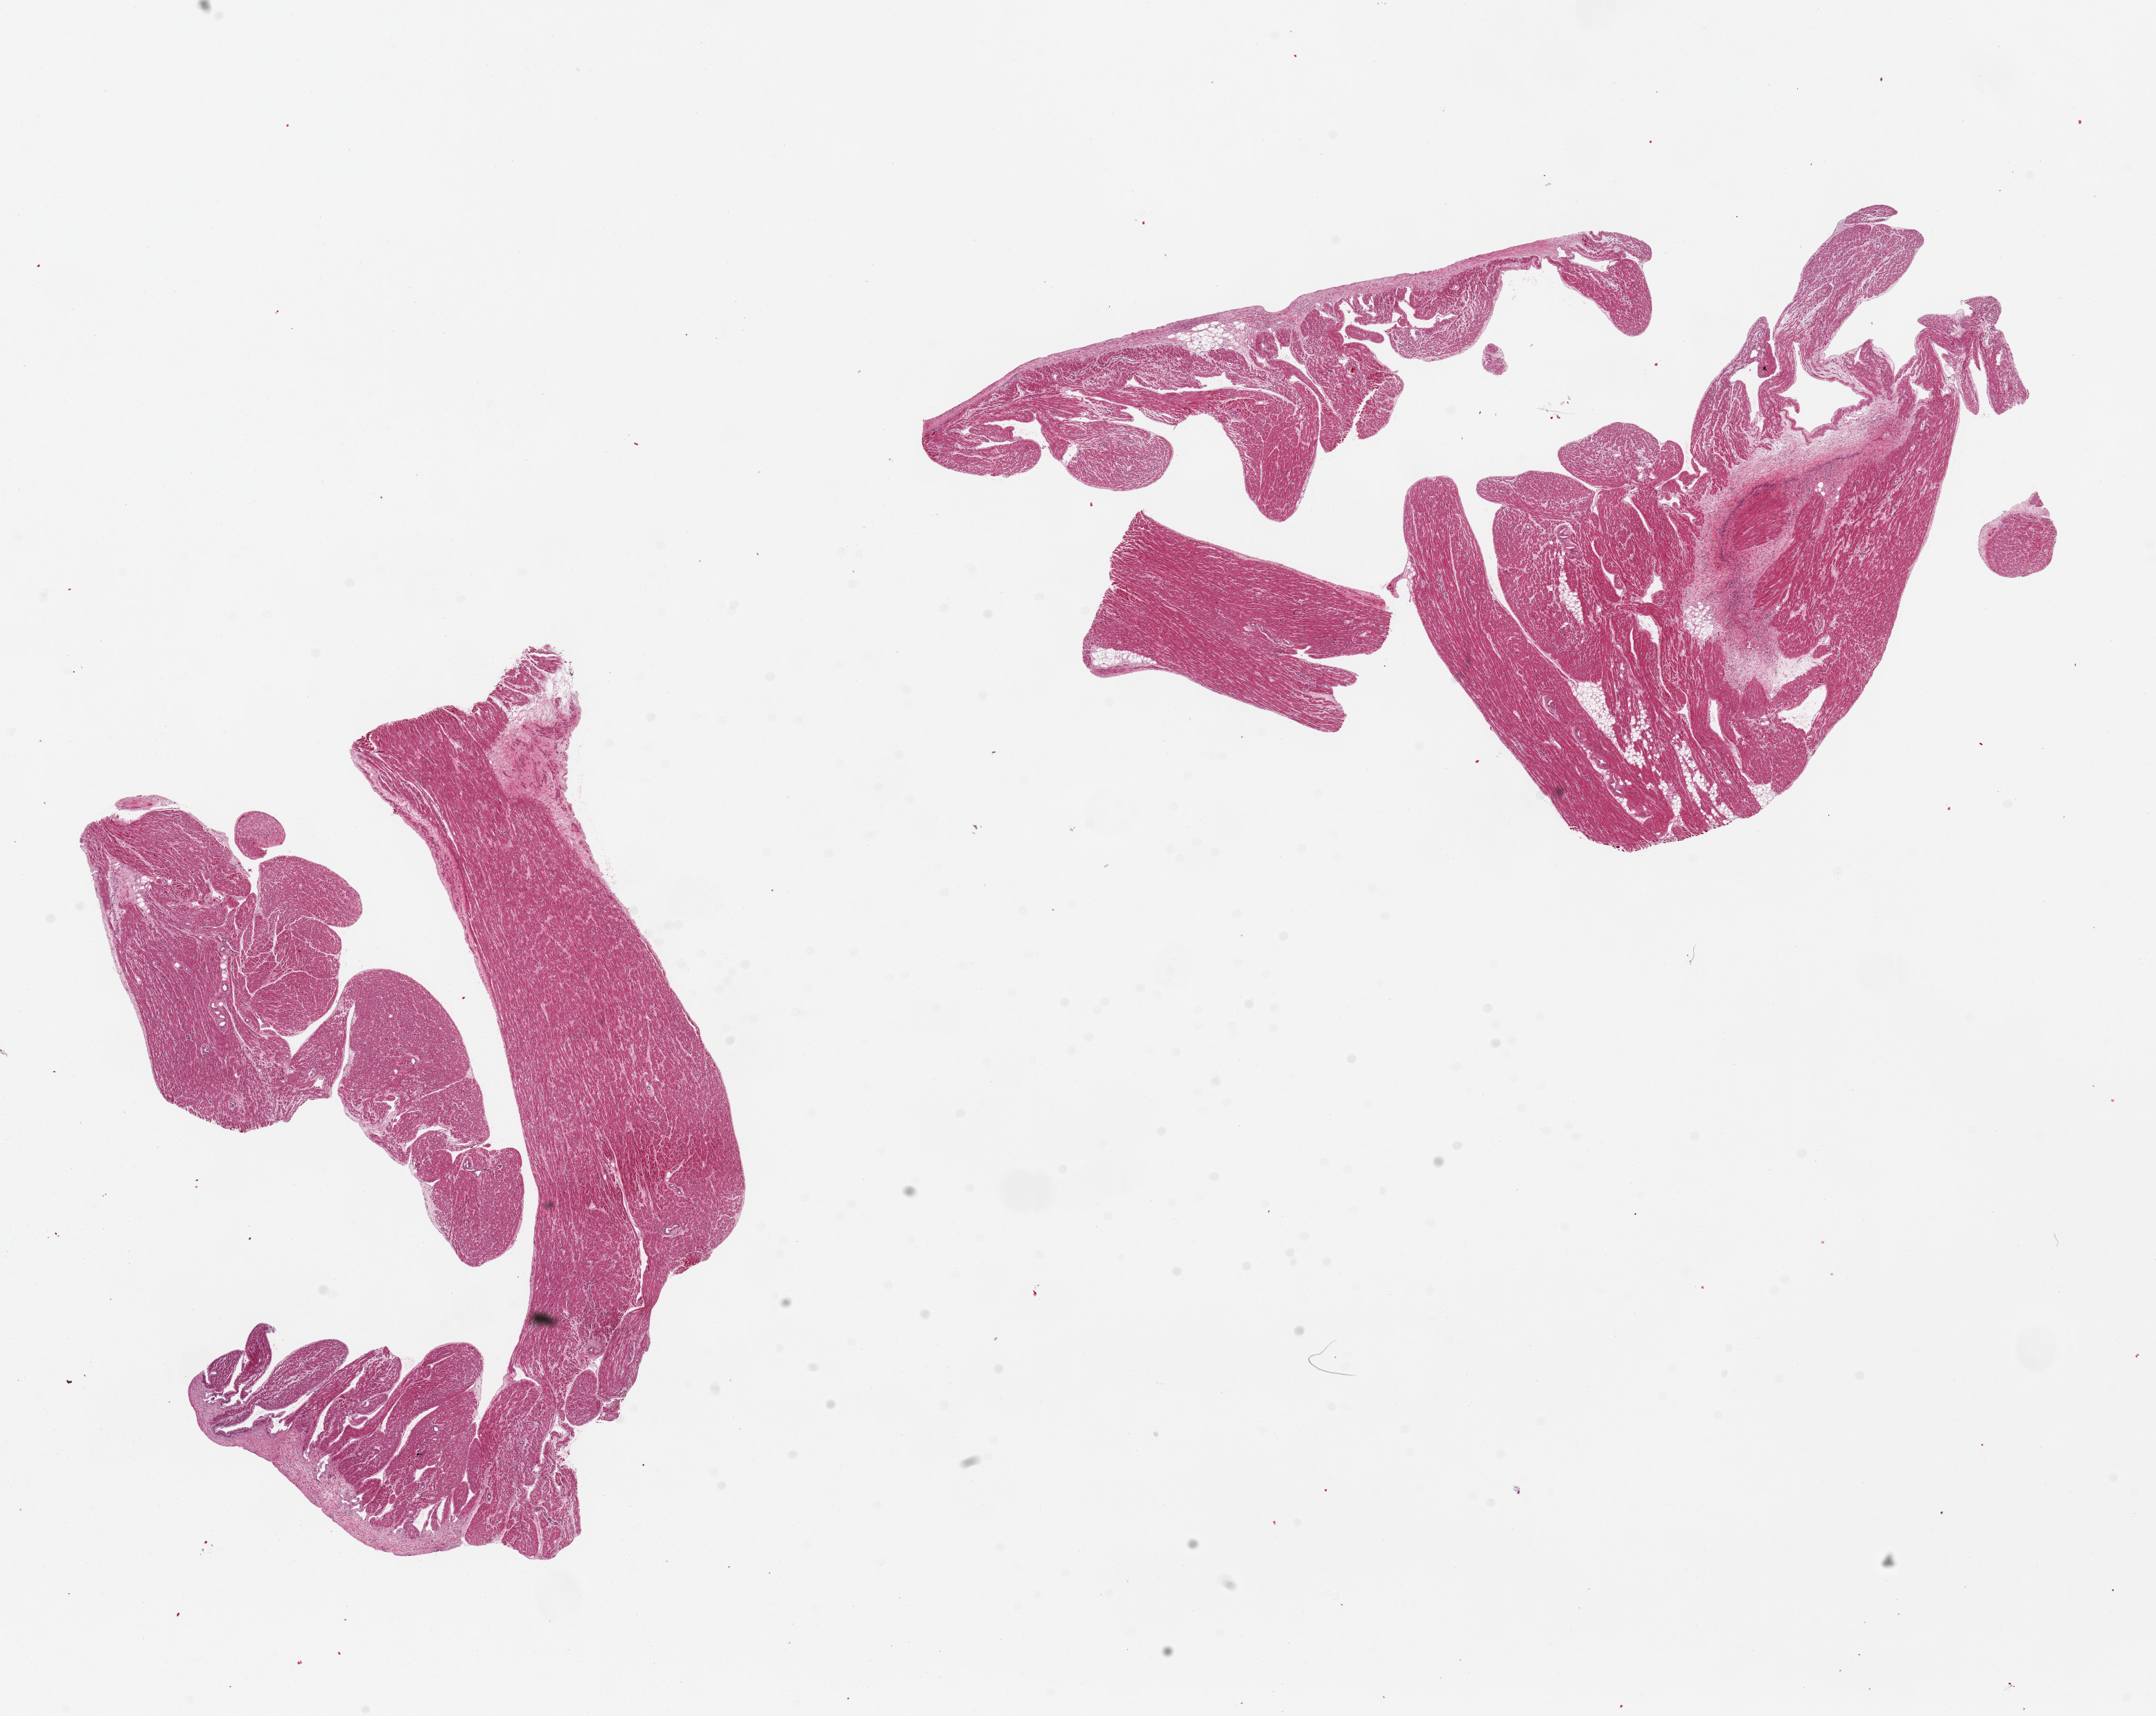
Digitized H&E-stained section — shown as a low-resolution overview of the whole scanned area (about 24.6 x 19.6 mm, acquisition: 20x scan). PAXgene-fixed paraffin-embedded (PFPE) section. Section of auricular appendage (target tissue). Donor tissue sample. Donor sex: female.
• pathologist's review note for this sample: 2 pieces, 10x7 & 13x7mm